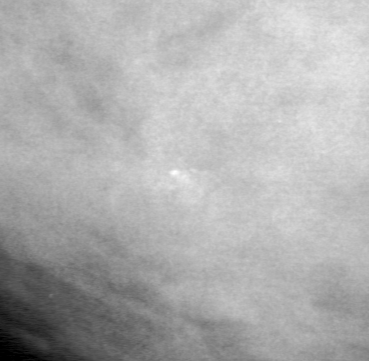
Region of interest cut from a scanned film mammogram (one marked finding), left breast, MLO view, BI-RADS breast density category 4 (scale 1–4).
Calcifications, morphology amorphous, distribution clustered; BI-RADS assessment category 4; subtlety rating 2 on a 1 (subtle) to 5 (obvious) scale; pathology (as recorded): benign.